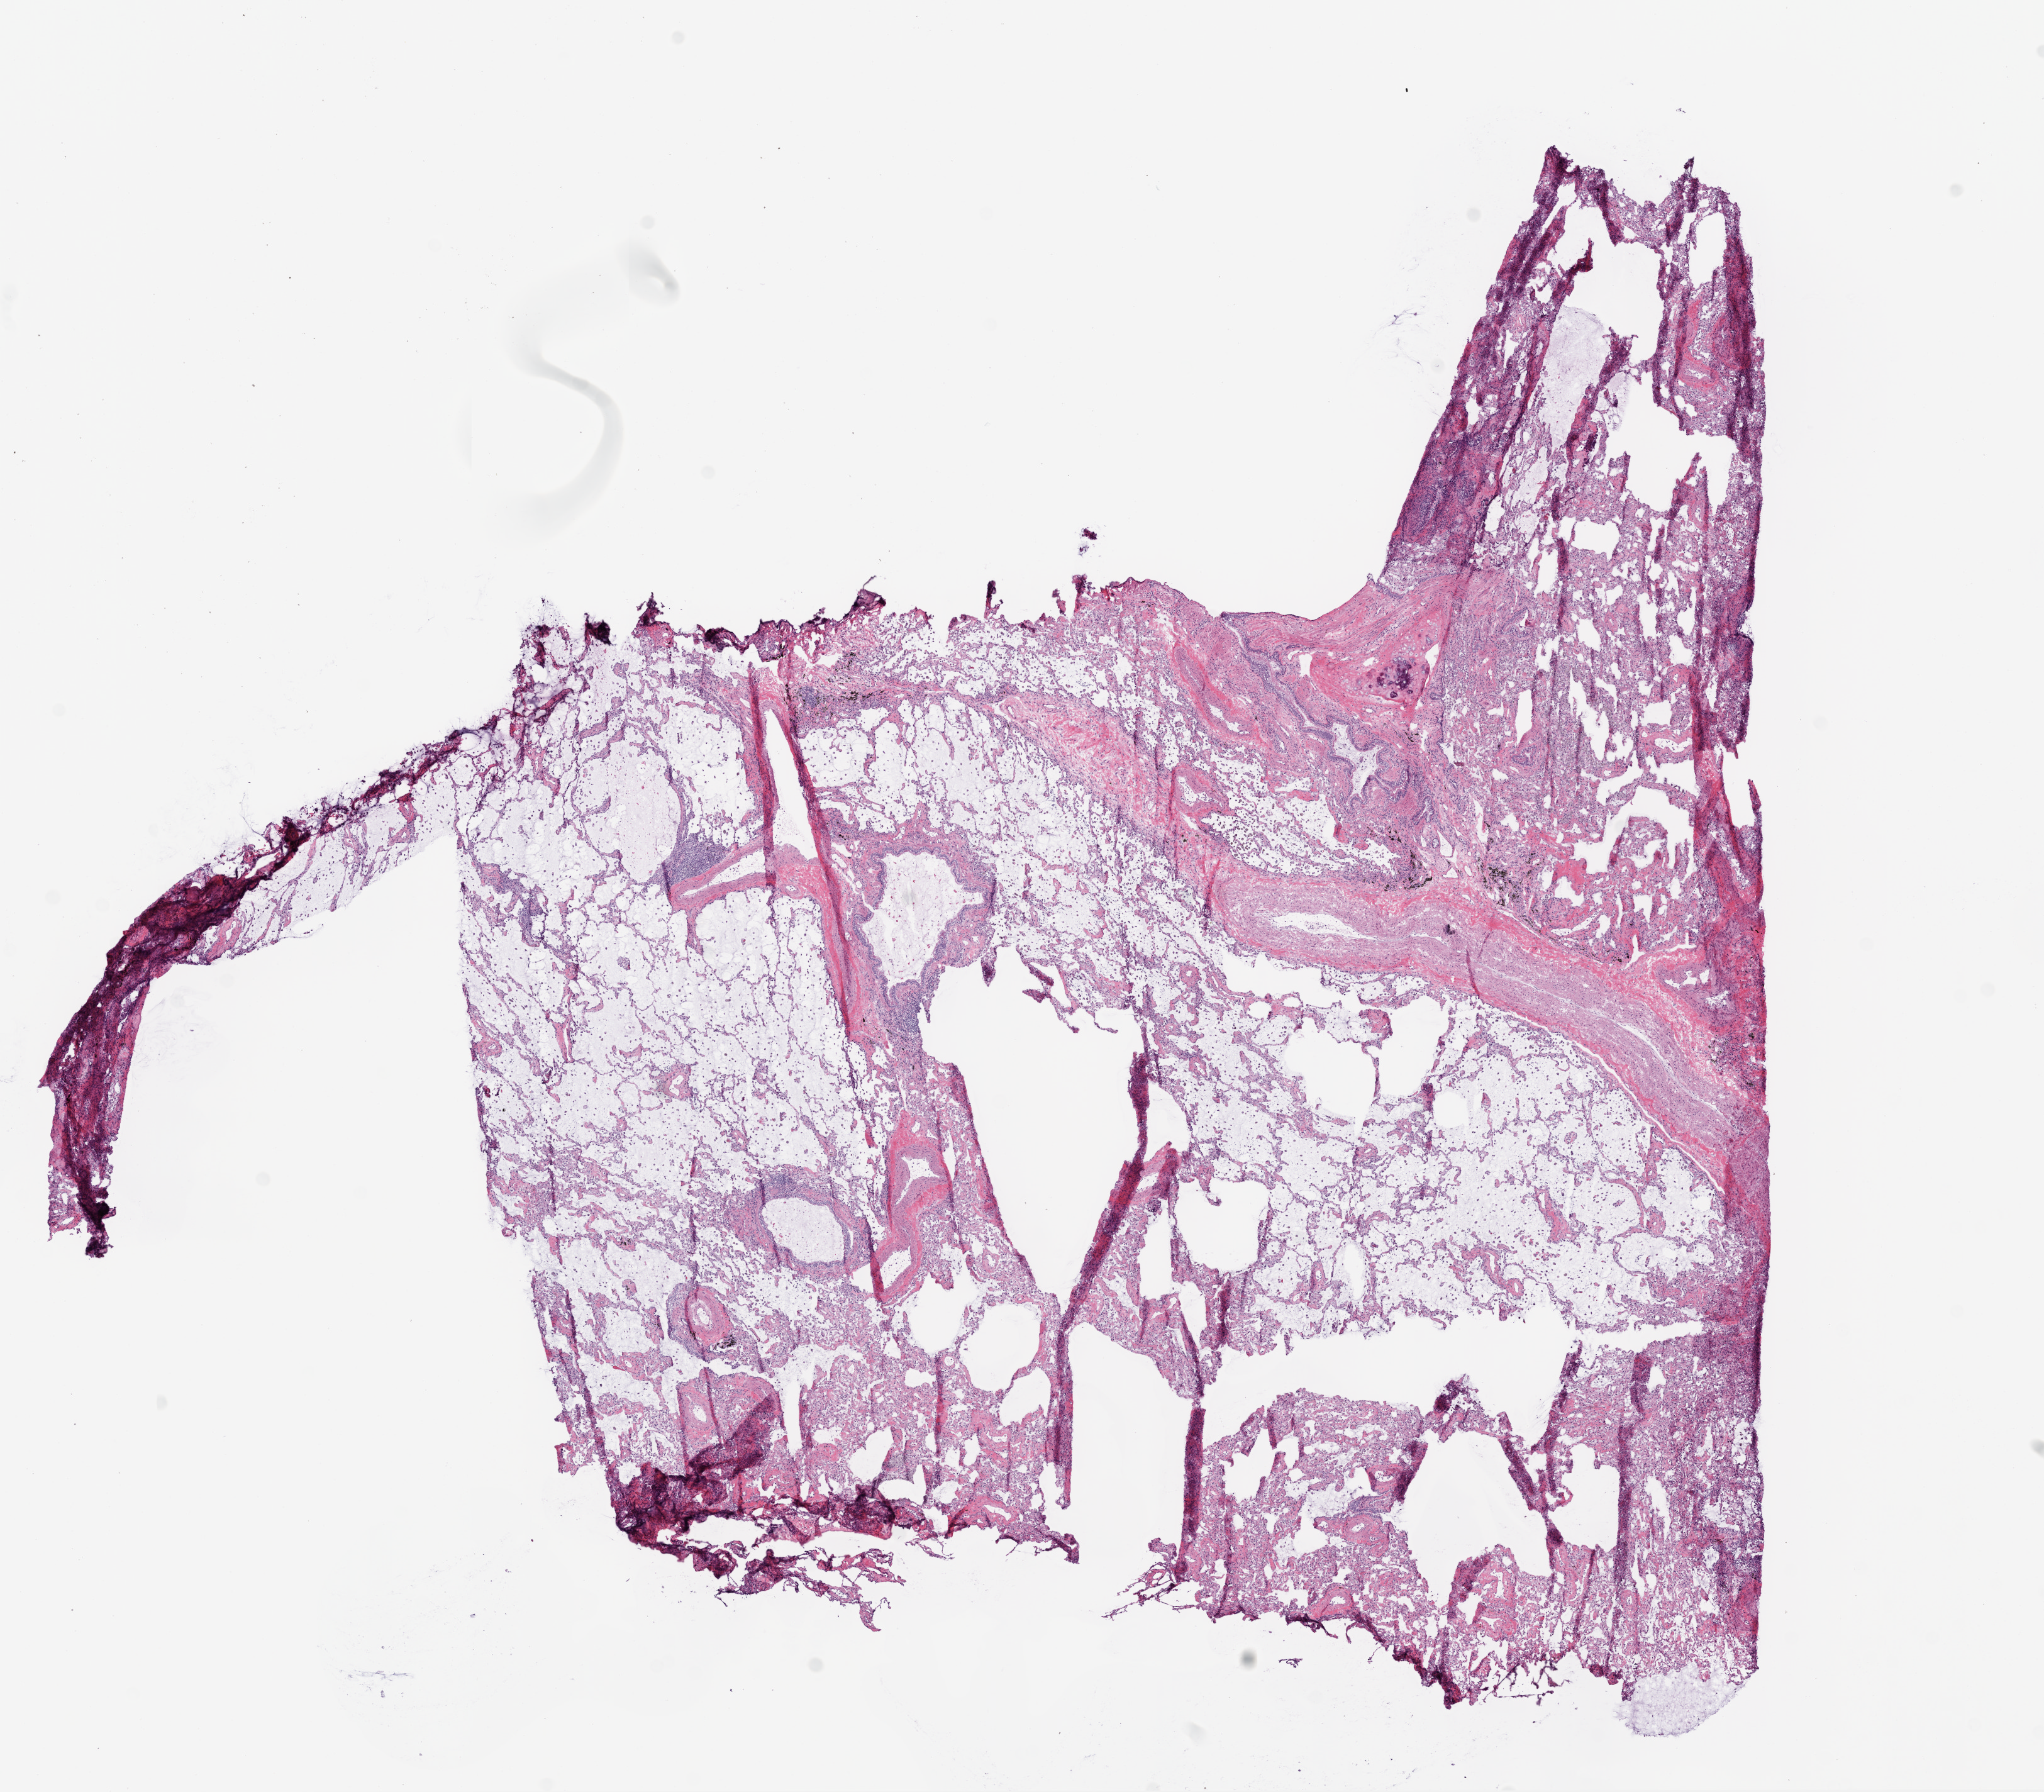
Digitized H&E-stained tissue section (whole slide) — low-resolution overview of the scanned area, about 13.0 x 11.4 mm, frozen section from the bottom of the tissue portion, sample: solid tissue normal (non-tumour tissue), lung. Female, age 64 years at initial diagnosis.
* this section: solid tissue normal sample (biorepository sample class)
* patient diagnosis: Squamous cell carcinoma, NOS